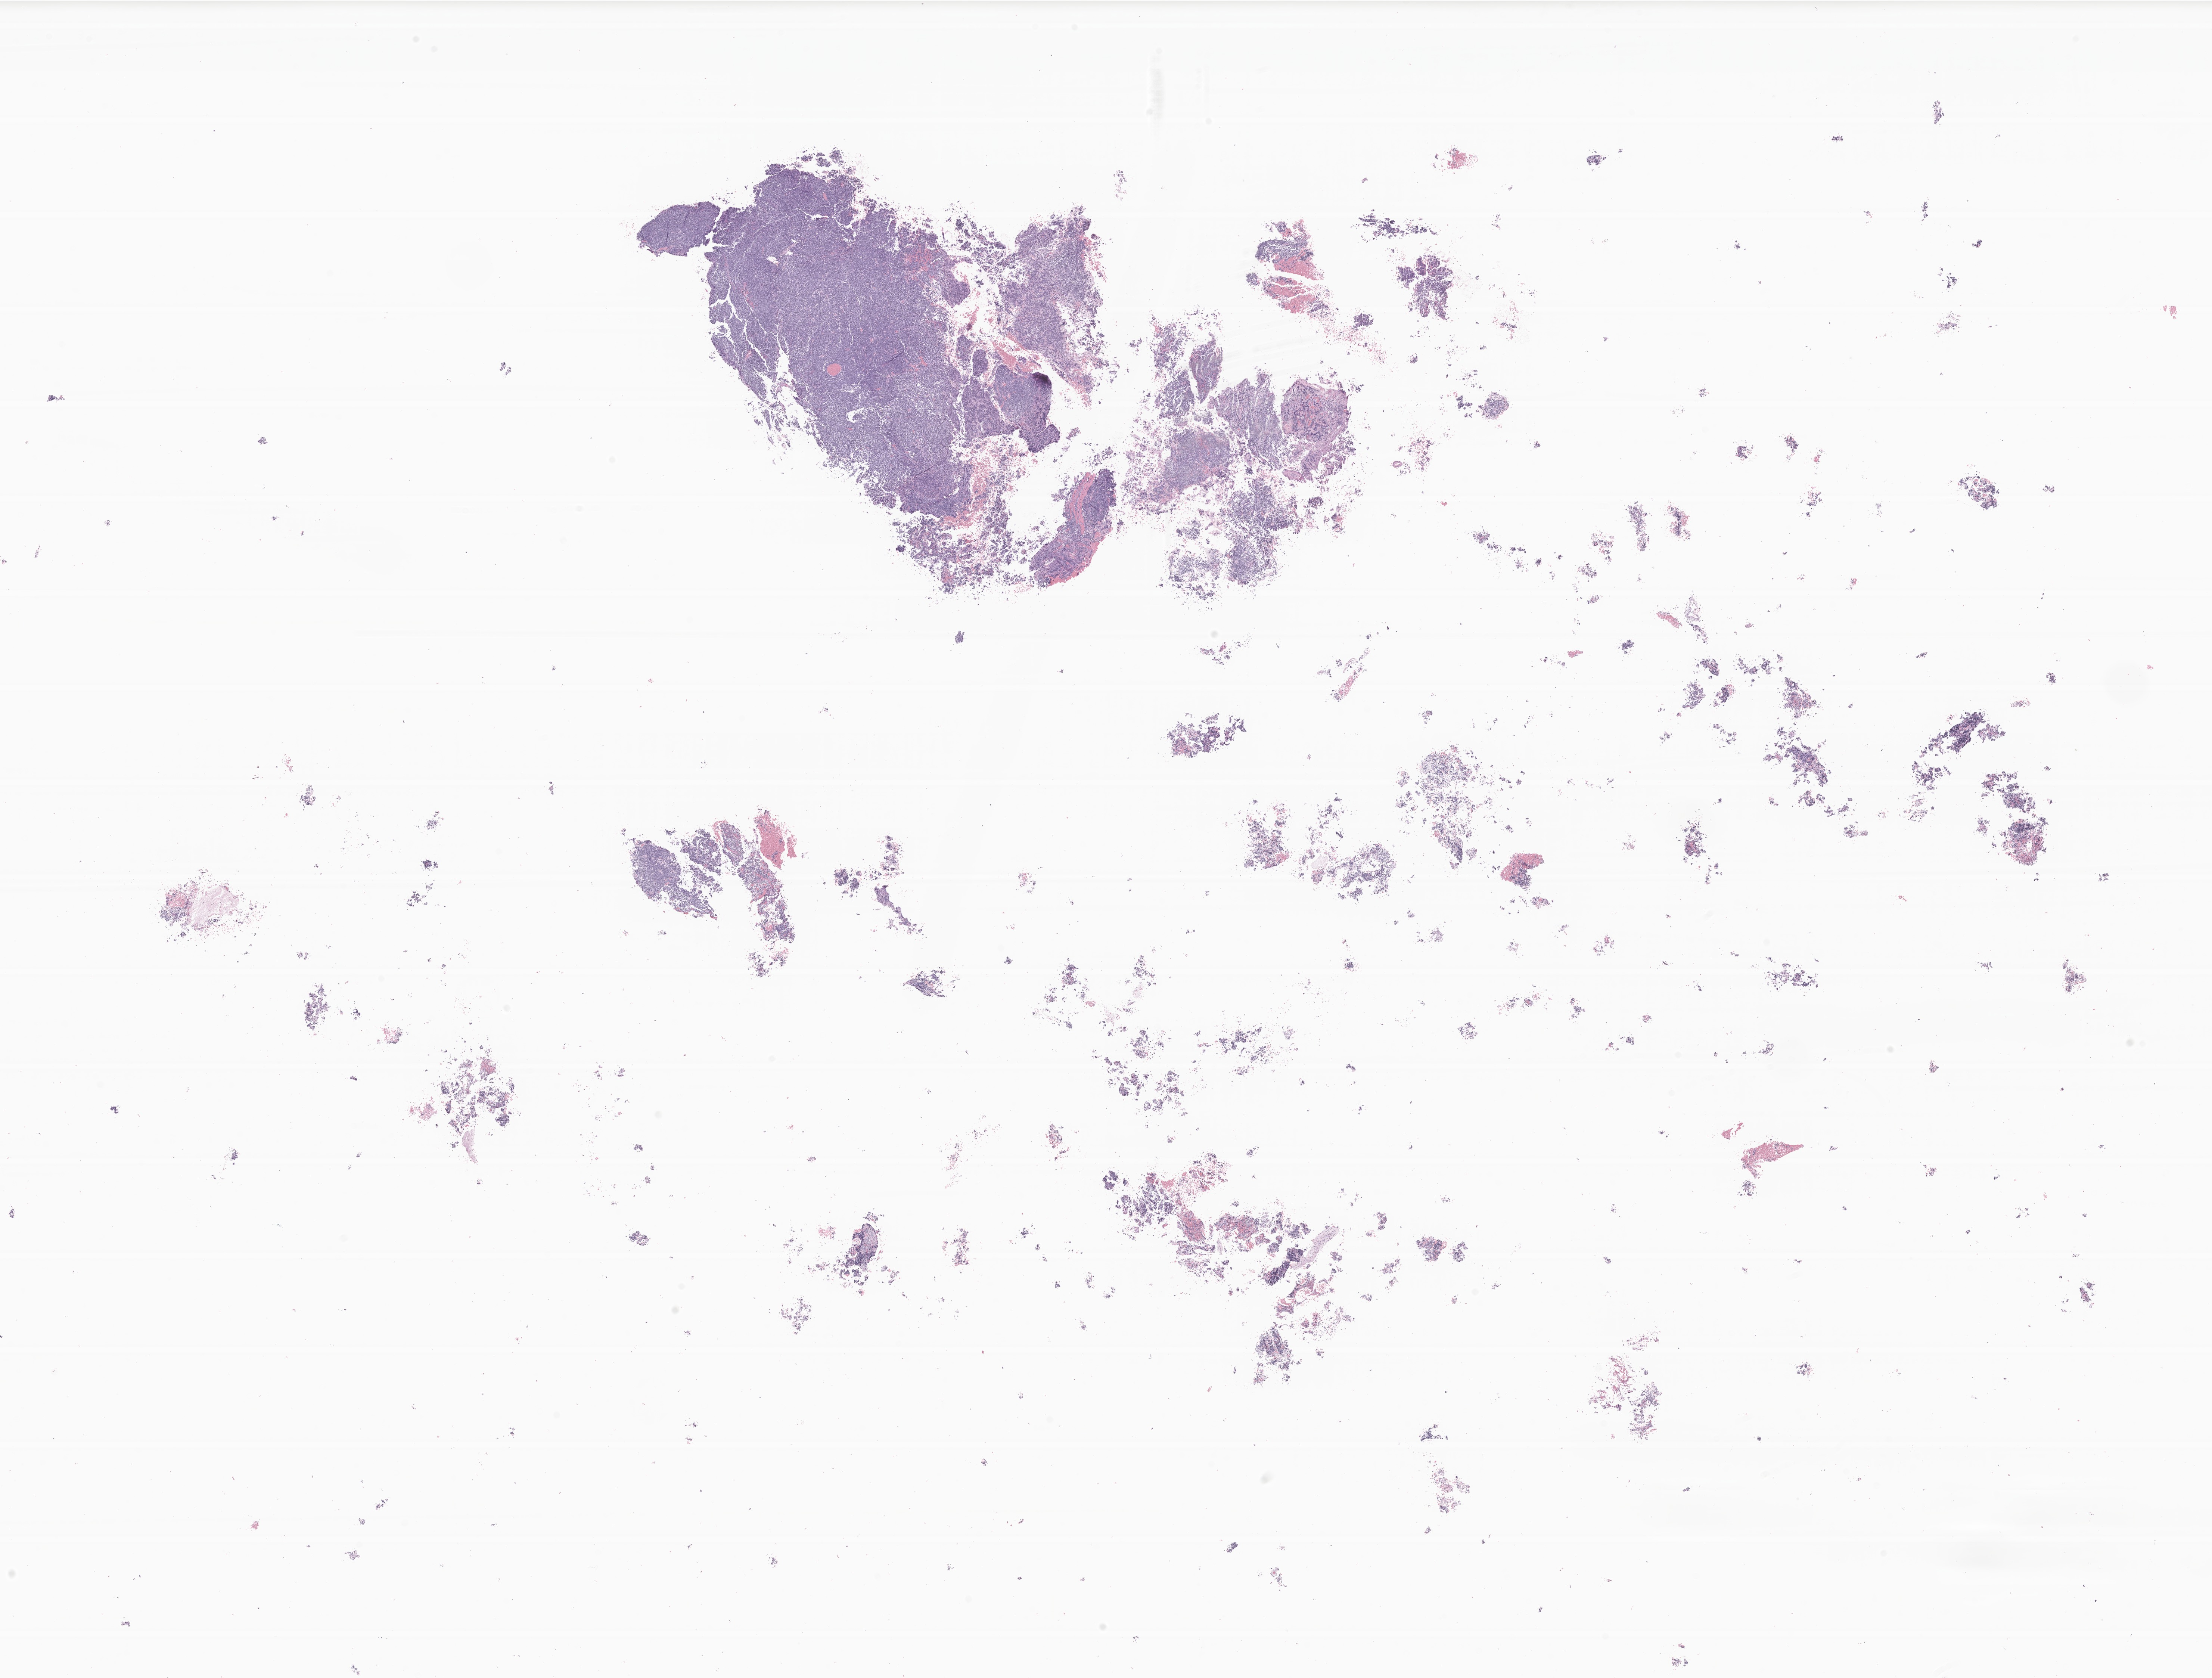
Whole-slide image, hematoxylin and eosin (H&E) stain of tumor tissue from the brain — low-resolution overview of the scanned area, about 25.0 x 18.9 mm; FFPE section. Patient: male, age 185 months (15 years 5 months).
Recorded diagnosis: Medulloblastoma, NOS.